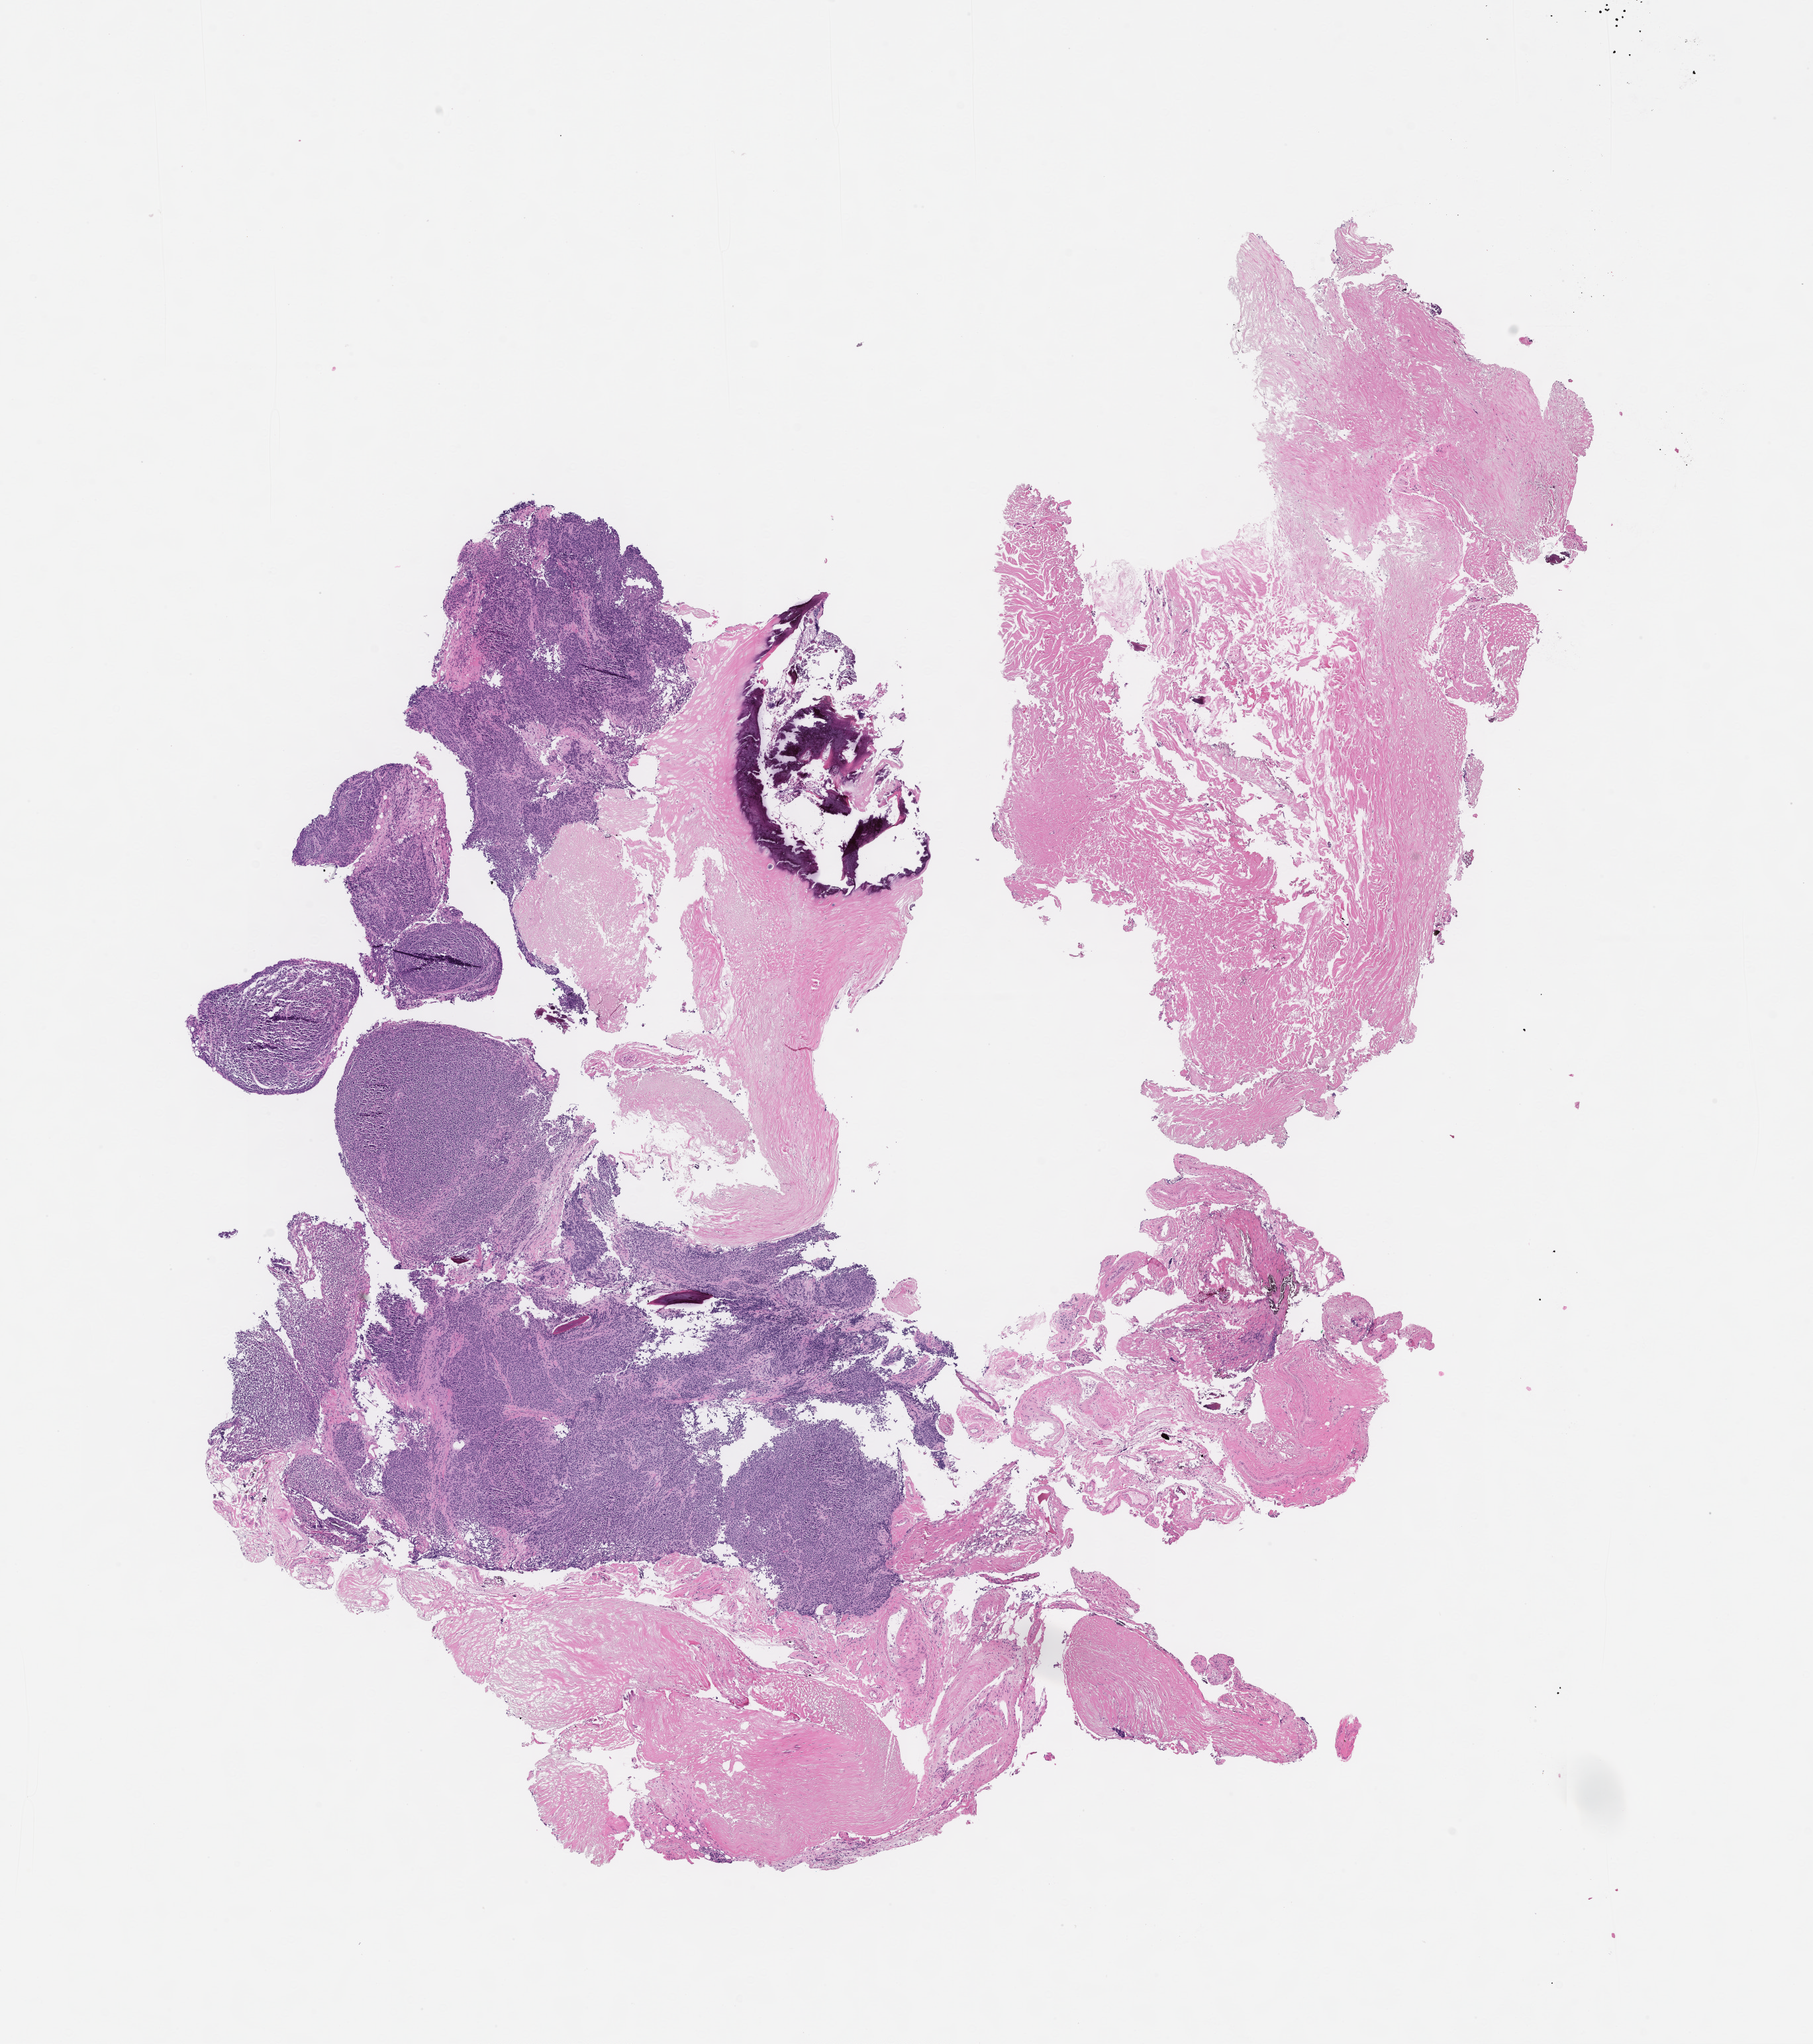
Whole-slide image, hematoxylin and eosin (H&E) stain — shown as a low-resolution overview of the whole scanned area (about 11.1 x 12.5 mm), formalin-fixed paraffin-embedded section, tissue site: bone marrow. Male patient.
This section: primary tumor. Diagnosis: Plasma Cell Myeloma.